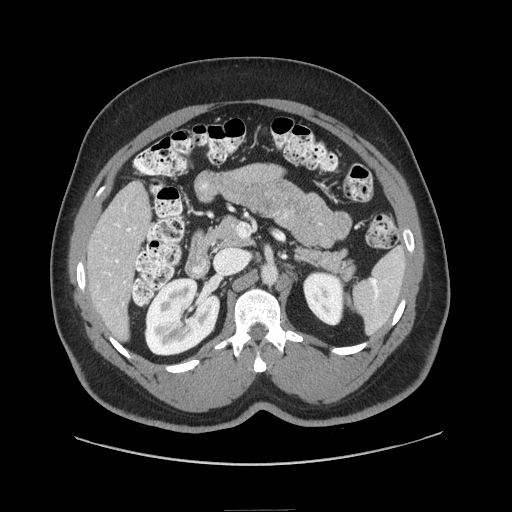
Contrast-enhanced abdominal CT (liver protocol), one axial slice. Position 31 of 87 along the scan axis. Soft-tissue window (W 400 / L 40 HU). 512 × 512 image matrix, field of view 440 × 440 mm. From the clinical record (not read from this slice): diagnosis: hepatocellular carcinoma (patient treated with transarterial chemoembolisation; whether this scan precedes or follows treatment is not stated here); TNM stage (as recorded): Stage-II; Child-Pugh class: A; tumour differentiation: moderately differentiated; tumour nodularity: uninodular.
Structures marked on this image (semi-automatic segmentation, software-assisted and operator-edited):
- liver parenchyma outside the tumour (the mass and vessels are separate outlines, so this box may not span the whole liver): bounding box [x1, y1, x2, y2] px = [86, 180, 150, 340]
- liver vessels: [97, 204, 136, 305]